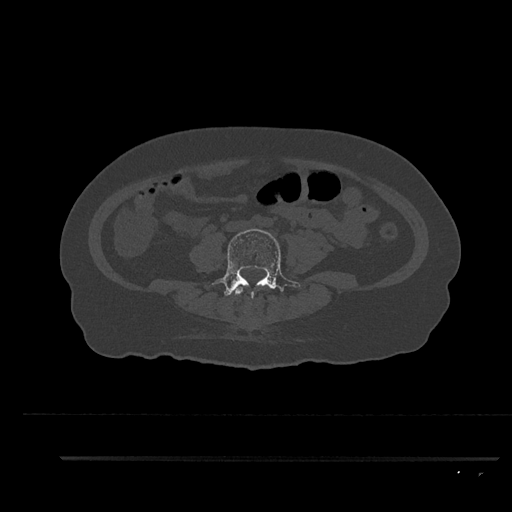
CT including the spine, one axial slice. Slice 32 of 797 in the series (ordered by position). Reconstruction kernel Br40s/3. Bone window (W 1800 / L 400 HU). 0.5 mm slice thickness. 512 × 512 image matrix. Patient: female, 44 years. Case-level facts recorded for this patient, not image findings: primary cancer: renal.
Structures marked on this image (semi-automatically segmented with operator editing):
- L3 vertebra: bounding box (x1, y1, x2, y2) in pixels: (235, 285, 265, 296)
- L4 vertebra: (209, 229, 300, 302)